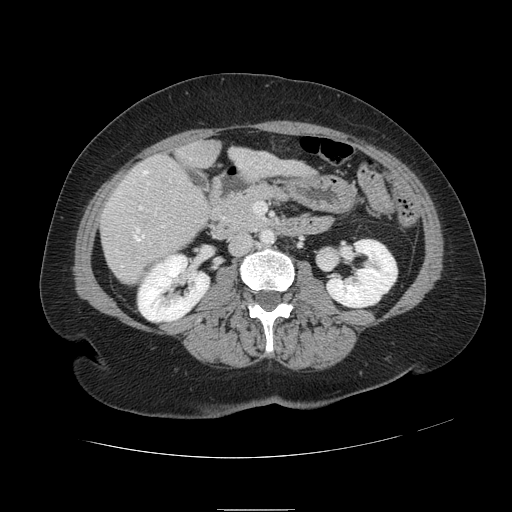
Contrast-enhanced abdominal CT, one axial slice; position 31 of 121 along the scan axis; soft-tissue window (W 400 / L 40 HU); 512 × 512 image matrix, field of view 400 × 400 mm. Female patient, age 52 years. Case-level facts recorded for this patient, not image findings: diagnosis: colorectal cancer liver metastases, imaged before liver resection; multiple liver metastases: yes; largest metastasis: 6.3 cm.
Structures marked on this image (manually delineated by an expert):
- hepatic veins: box from (x=121, y=167) to (x=271, y=267) px
- liver: (x=100, y=142)–(x=307, y=284)
- planned liver remnant (the part of the liver to remain after resection): (x=178, y=142)–(x=306, y=176)
- portal vein (with intrahepatic branches): (x=139, y=206)–(x=142, y=210)